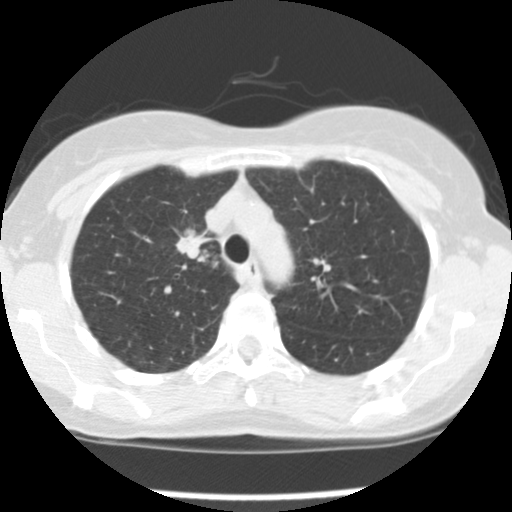
Low-dose screening chest CT, one axial slice; slice 117 of 157 in the series (ordered by position); reconstruction kernel STANDARD; 120 kVp; lung window (W 1500 / L -600 HU); 512 × 512 image matrix, field of view 282 × 282 mm.
Outlined on this slice (expert manual segmentation):
- lesion 1 (tumor, upper lobe of right lung): box from (x=176, y=229) to (x=211, y=259) px